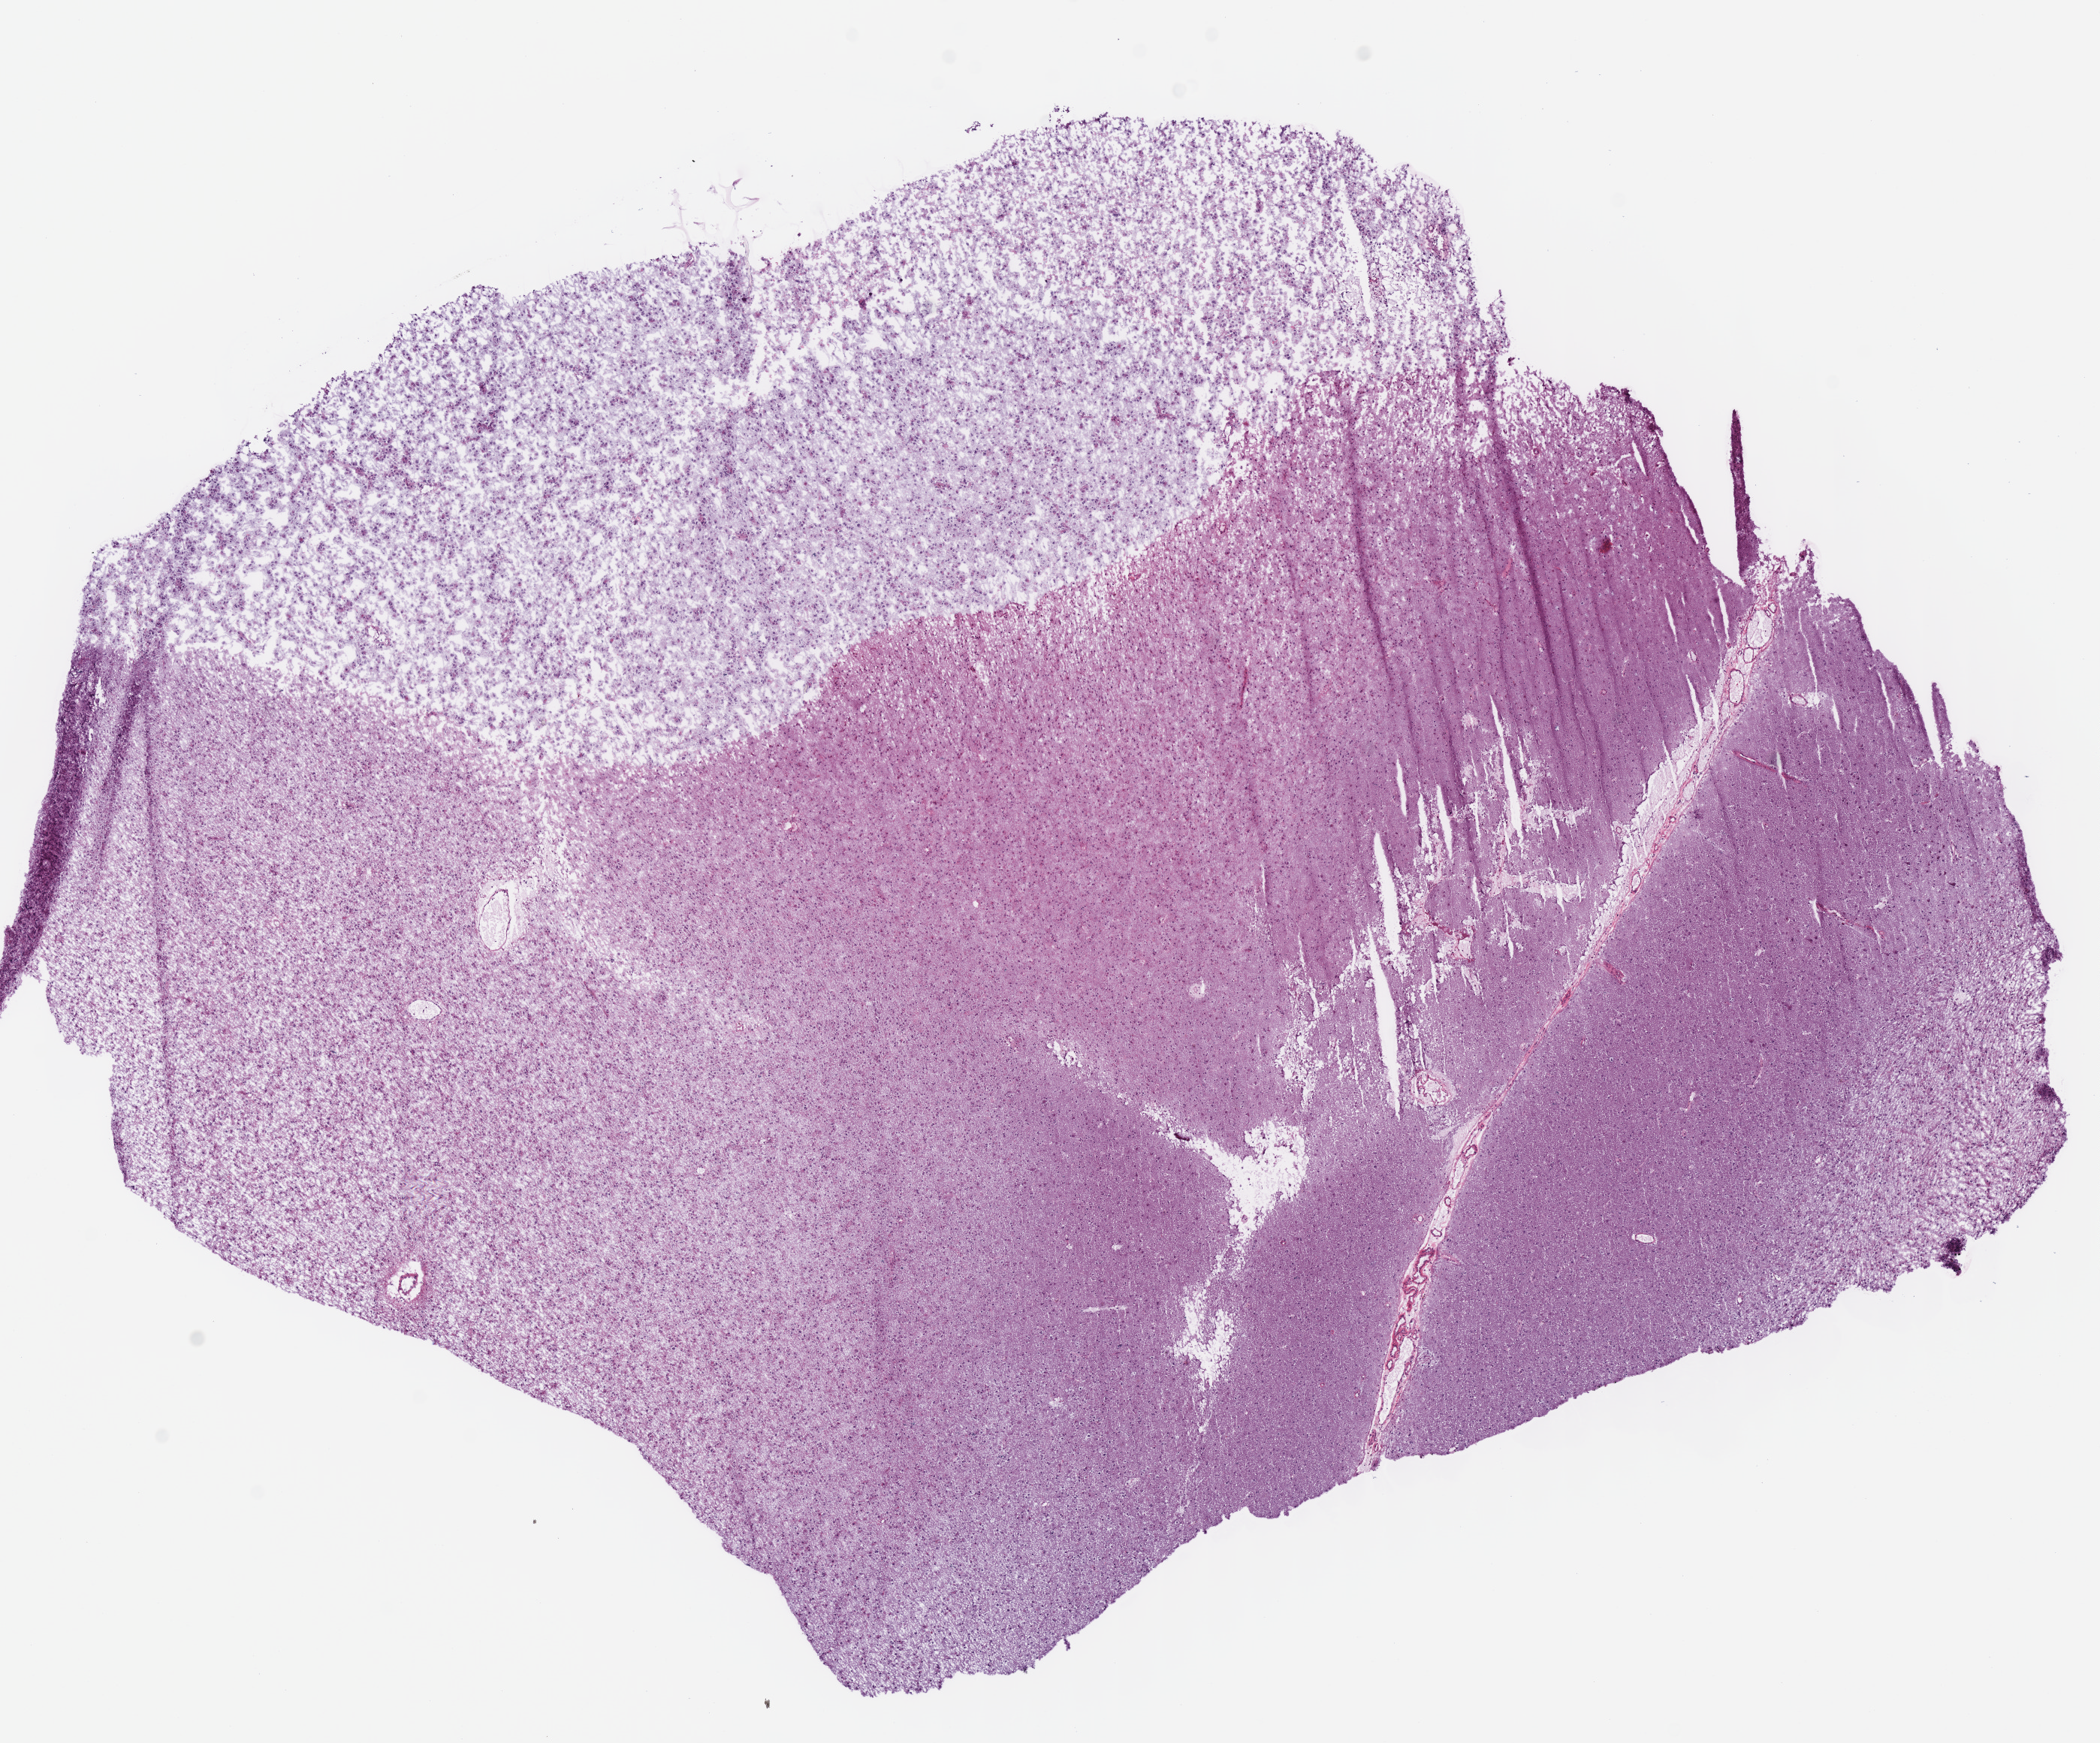
H&E whole-slide image, whole scanned area (about 11.0 x 9.1 mm) shown as a low-resolution overview; frozen section from the bottom of the tissue portion; sample: primary tumour, brain. Male patient; age at initial diagnosis 38 years. Histologic grade: G2 (moderately differentiated). Pathologist review of this section (percent, as recorded): tumour cells 100%, tumour nuclei 75%, normal cells 0%, stromal cells 0%, necrosis 0%.
Laterality: right. Diagnosis: Mixed glioma (cerebrum).